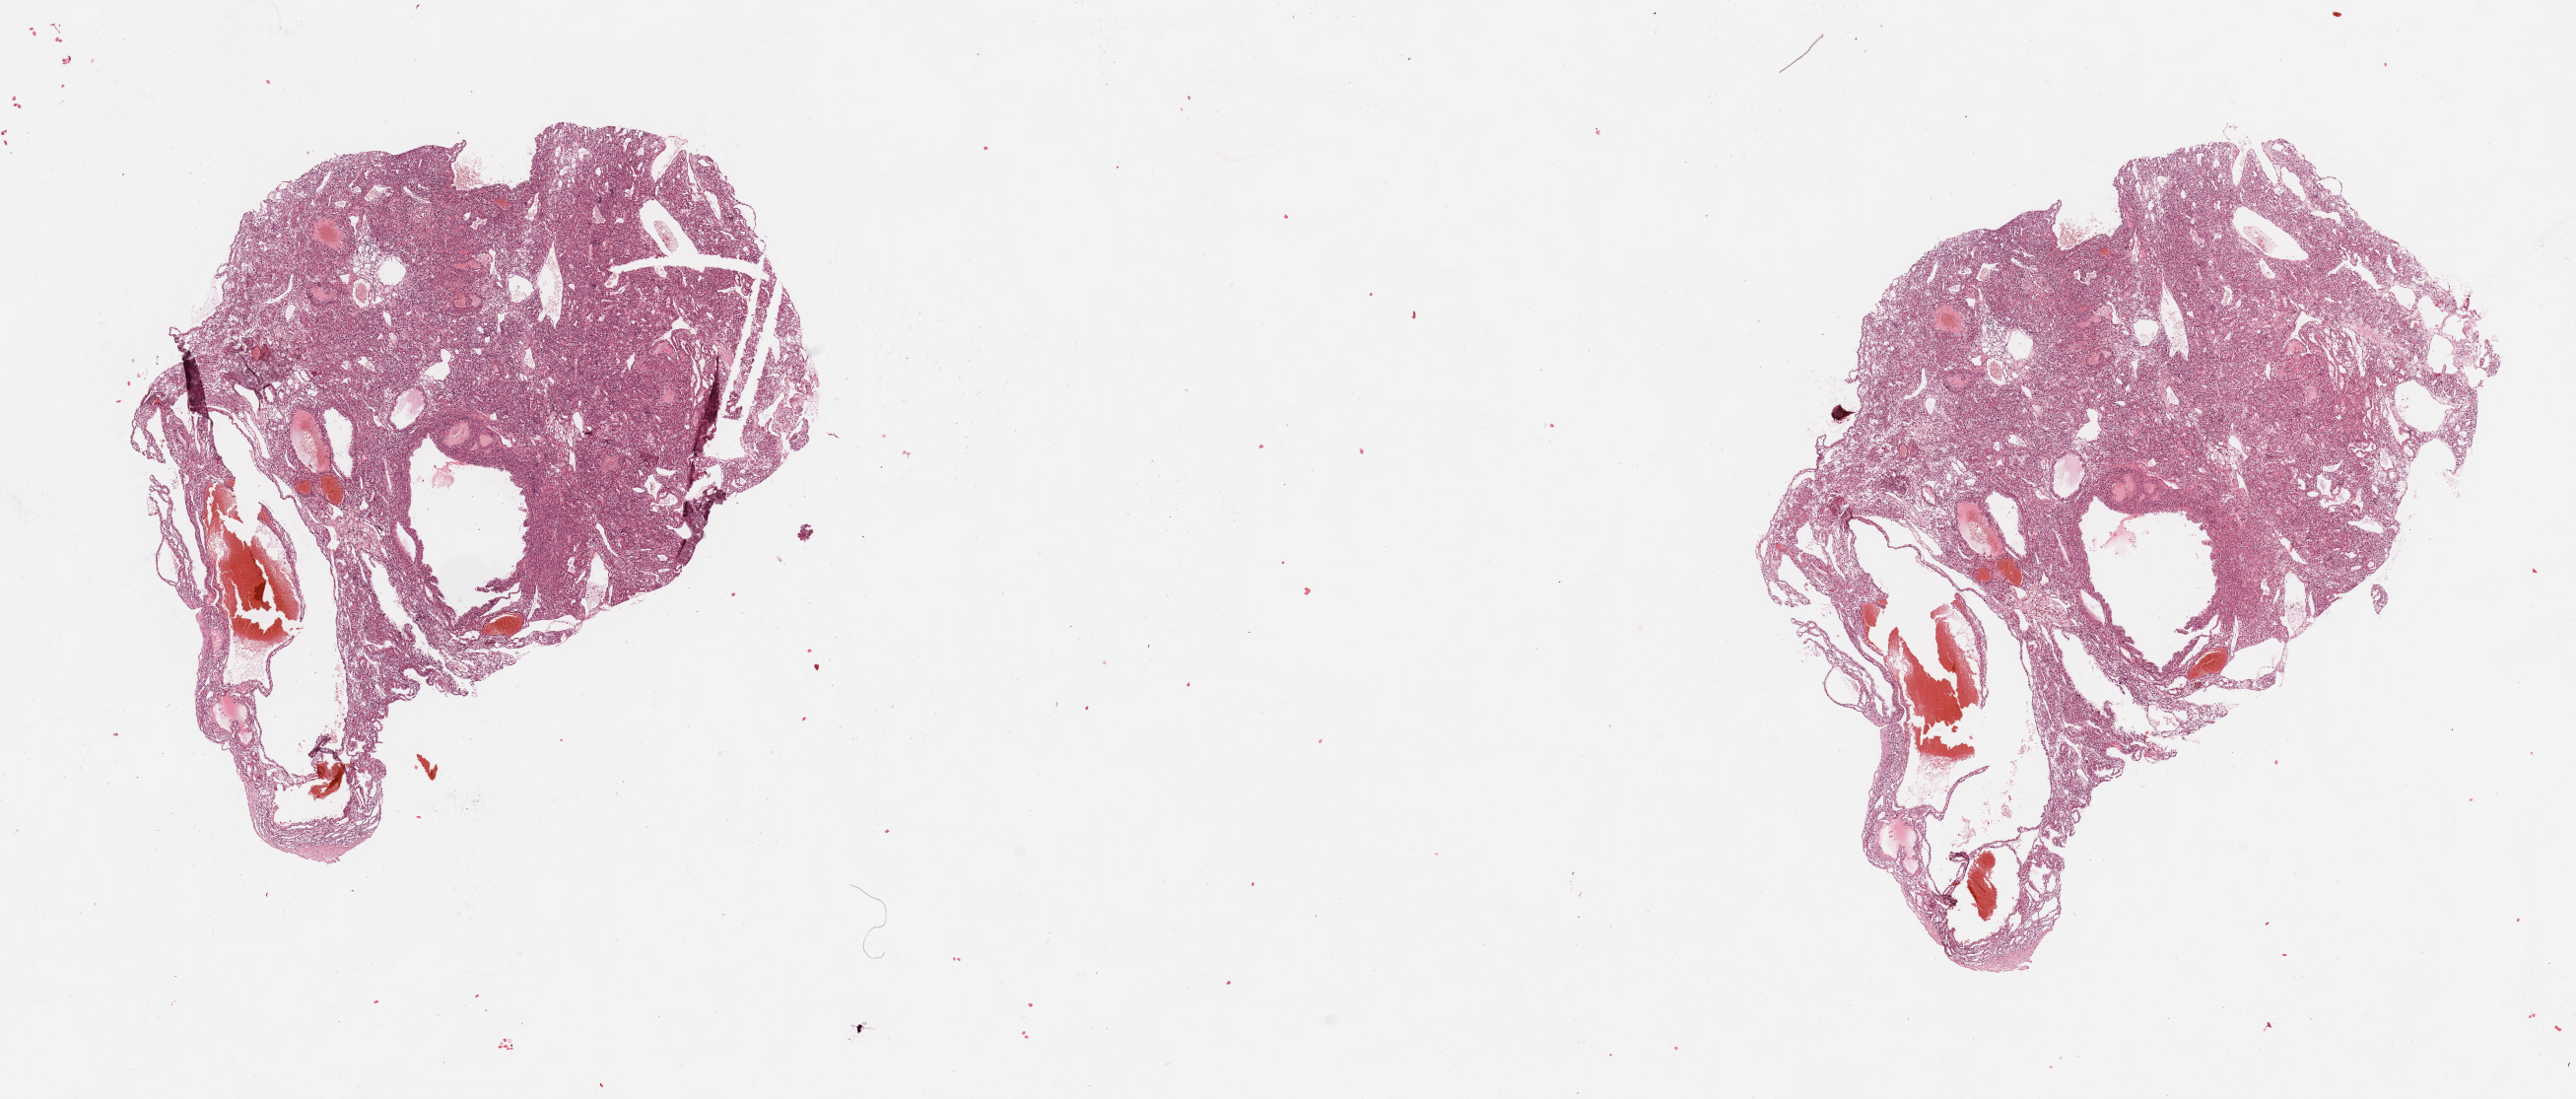
Whole-slide histology image, H&E, shown as a low-resolution overview of the whole scanned area (about 20.7 x 8.8 mm). Tumour tissue sample, sampled site: kidney. Male, 71 y/o. Histologic grade: G2 (moderately differentiated). Composition of this section per pathologist review: tumour nuclei 85%, necrosis 10%.
Diagnosis: Renal cell carcinoma, NOS. AJCC pathologic stage: III. Primary tumour site (as recorded): upper pole.